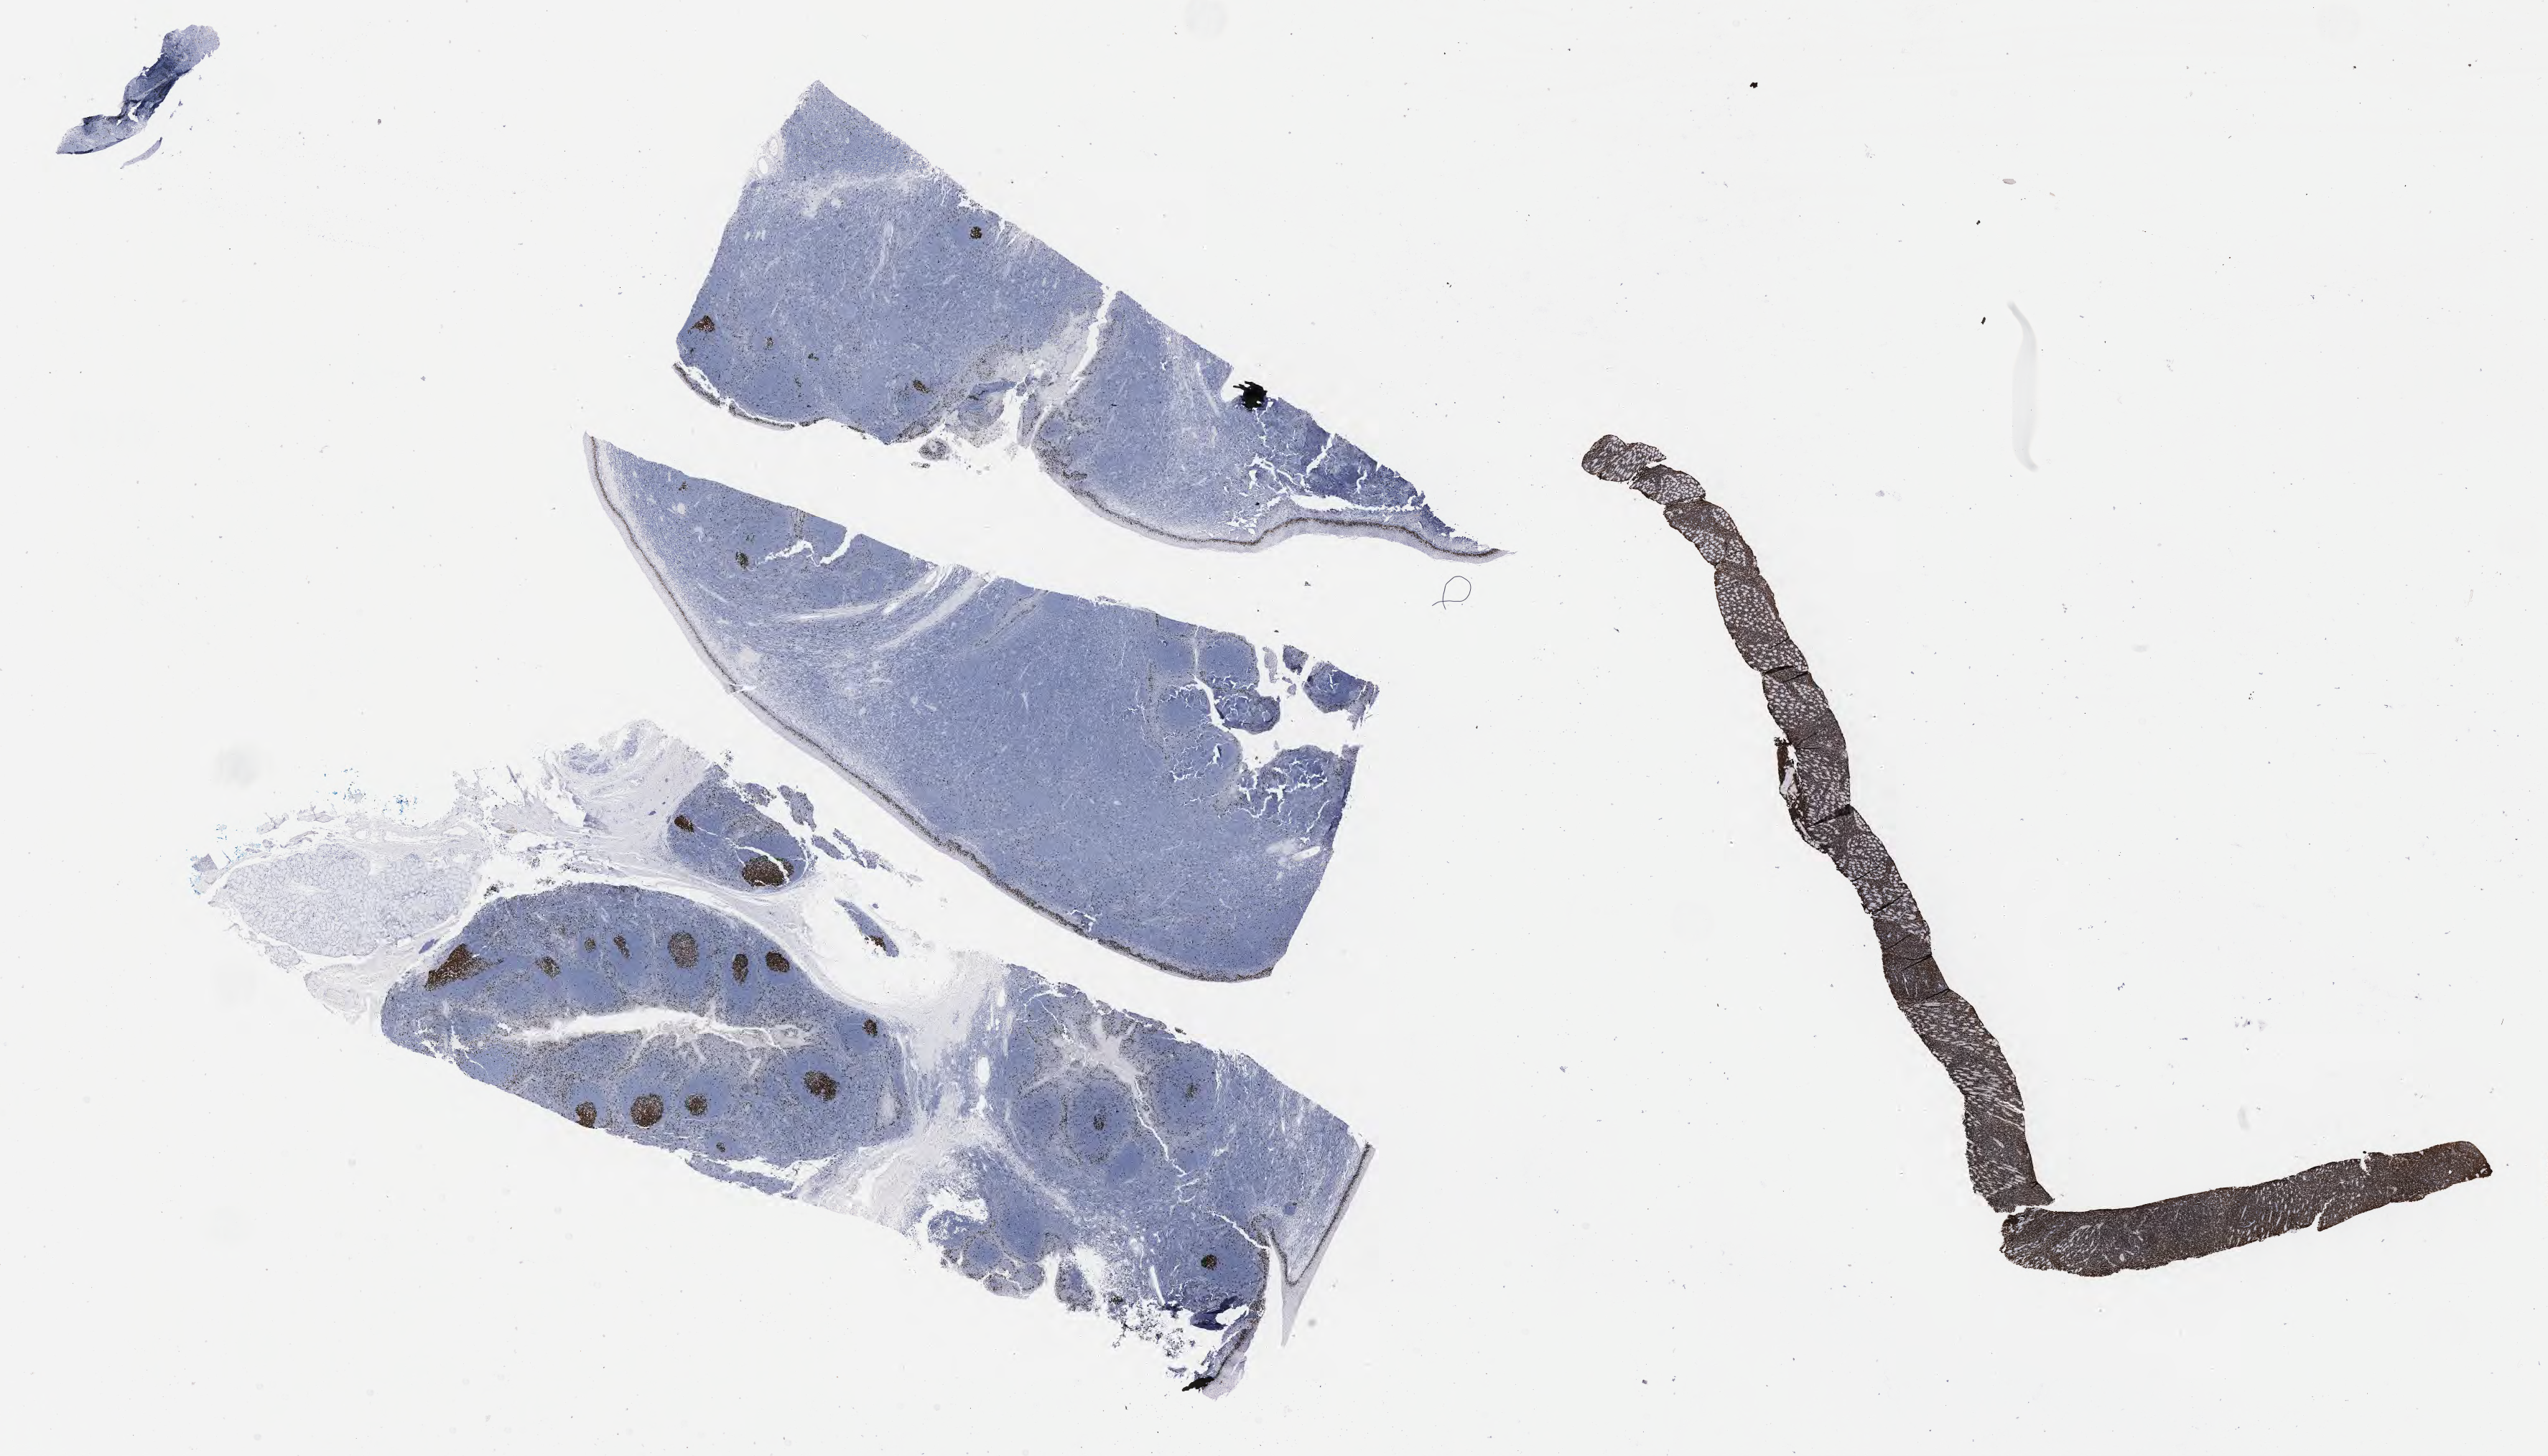
Immunohistochemistry (IHC) whole-slide image stained for Ki-67 — a low-resolution overview of the entire scanned area, about 28.7 x 16.4 mm, specimen: tumor tissue. Male patient; age at initial diagnosis 4 years.
Histologic diagnosis: Burkitt lymphoma, NOS.